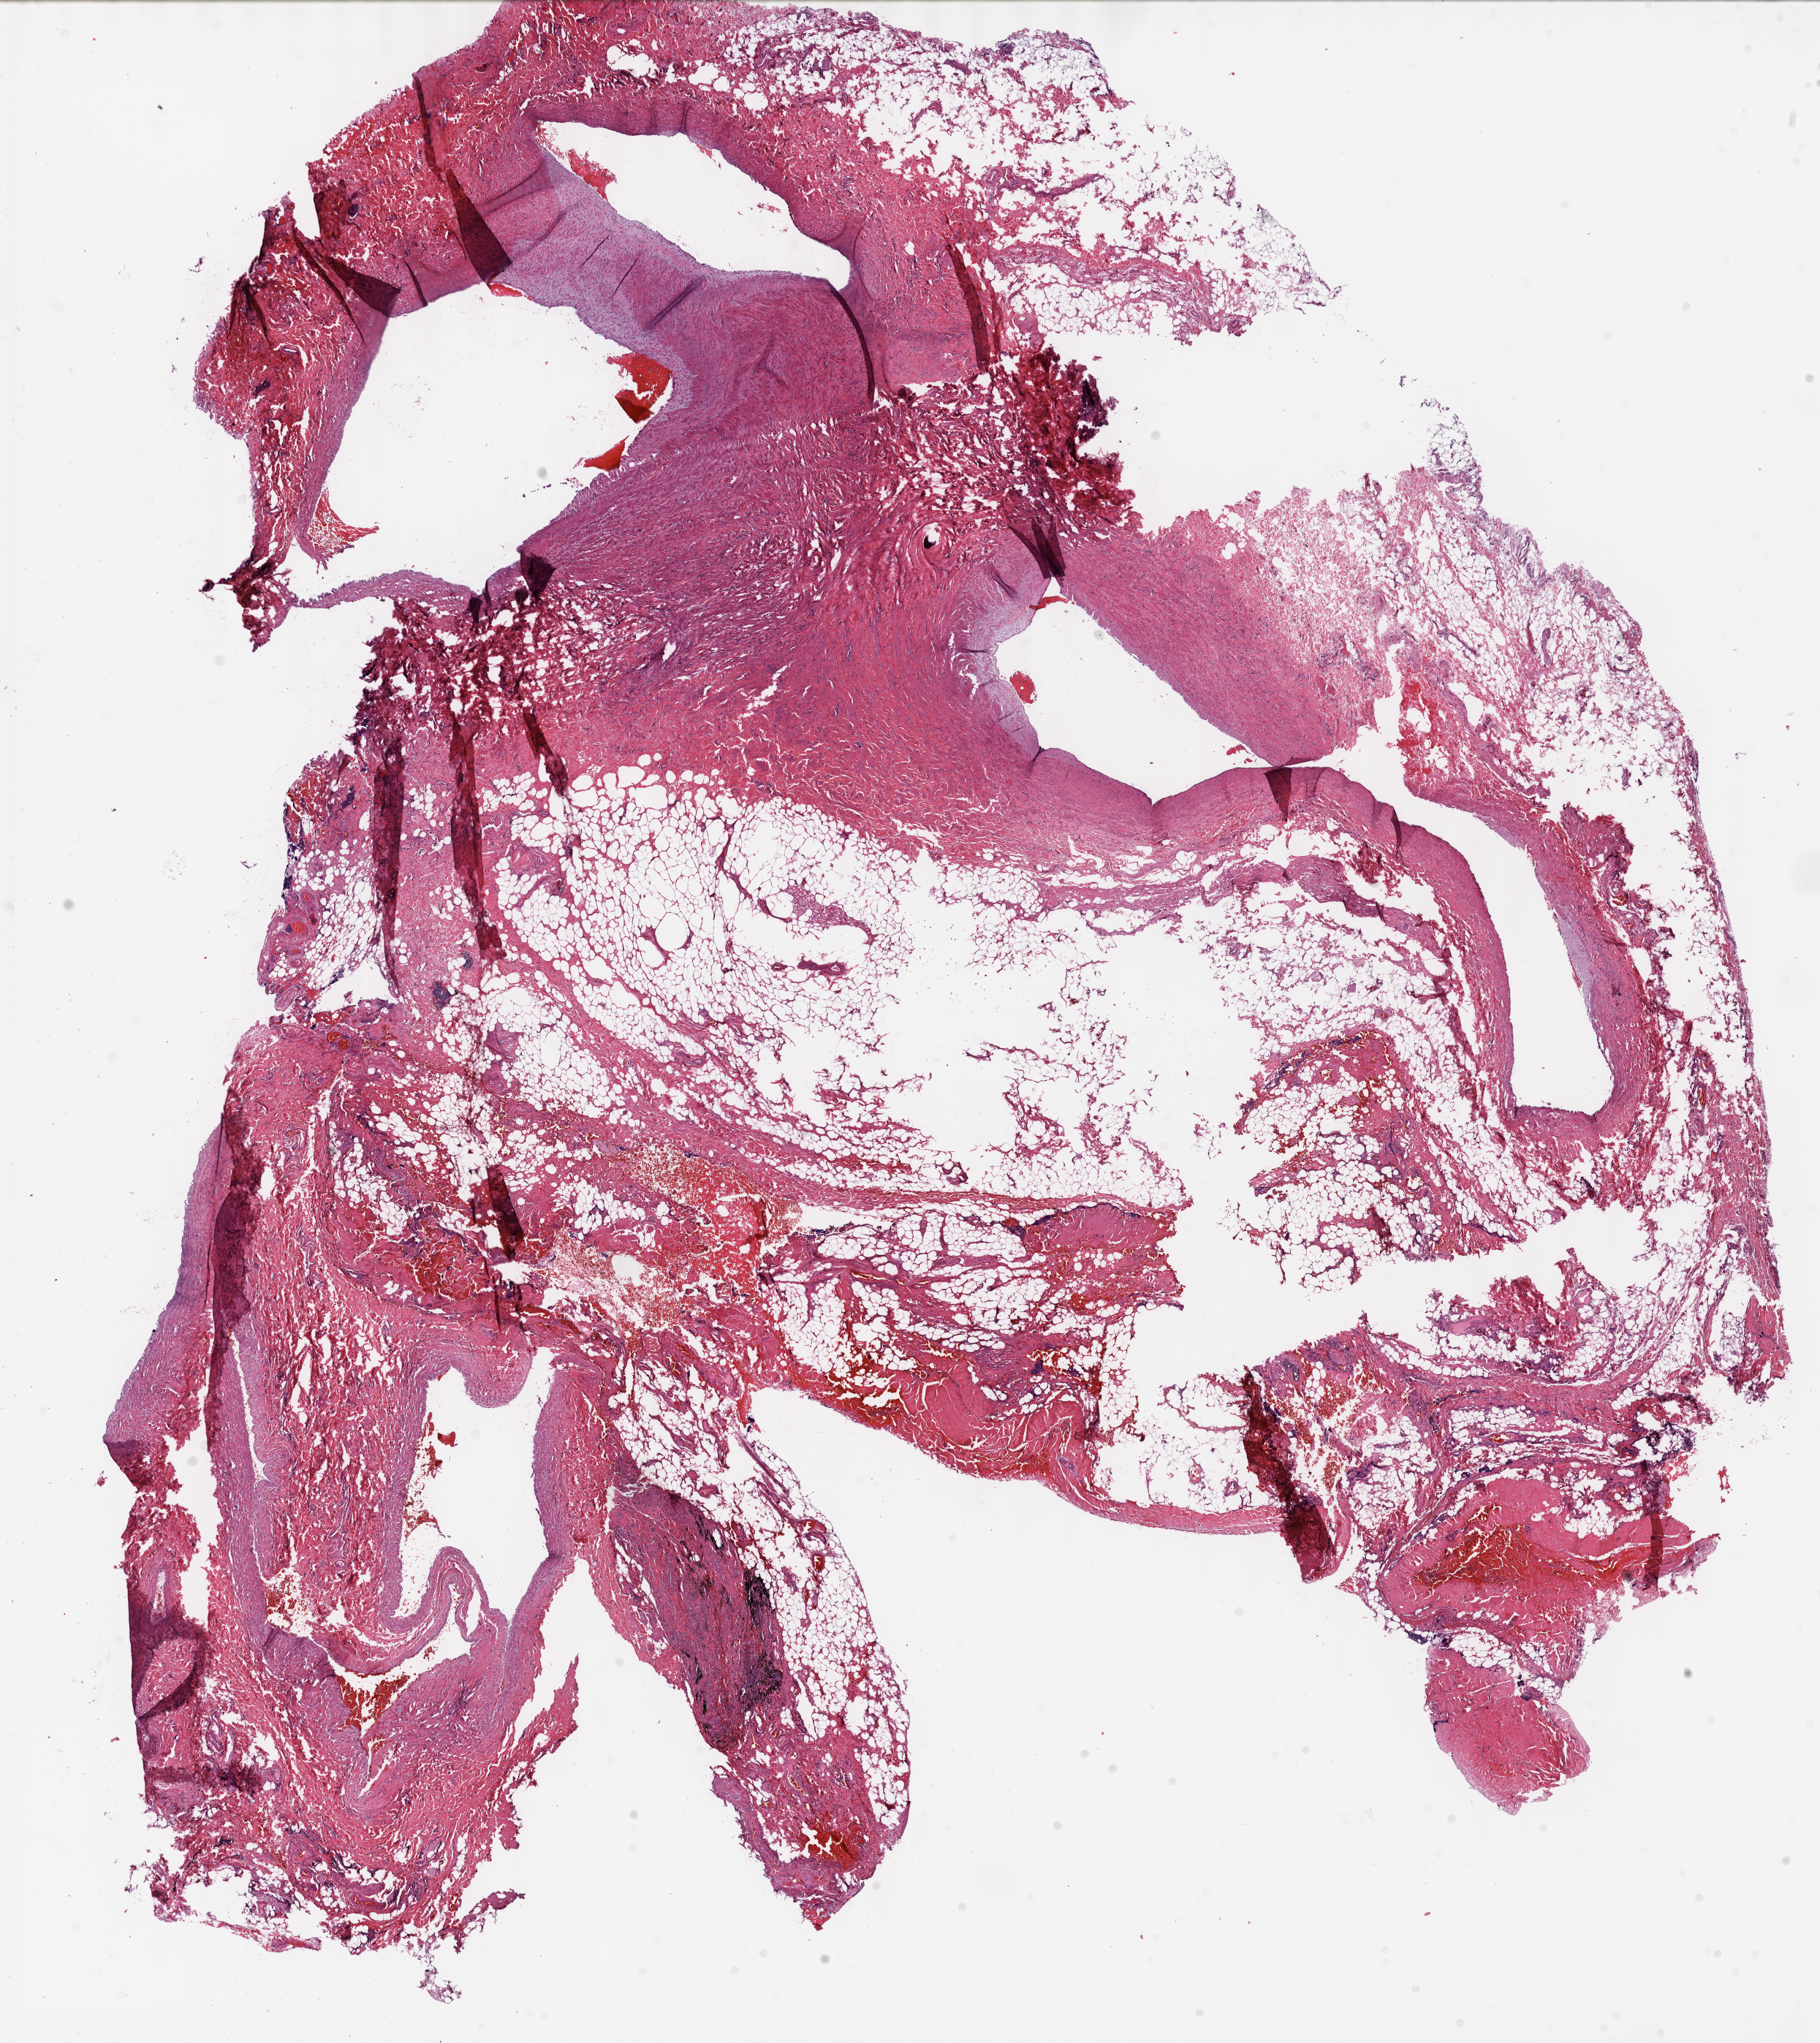
Whole-slide histology image, Hematoxylin and eosin (H&E) stained, shown as a low-resolution overview of the whole scanned area (about 20.1 x 22.6 mm, slide scanned at 40x). Formalin-fixed paraffin-embedded (FFPE) diagnostic section. Primary tumour sample from the lung. Male patient; age at initial diagnosis 66 years.
Histologic diagnosis: Squamous cell carcinoma, NOS (upper lobe, lung).